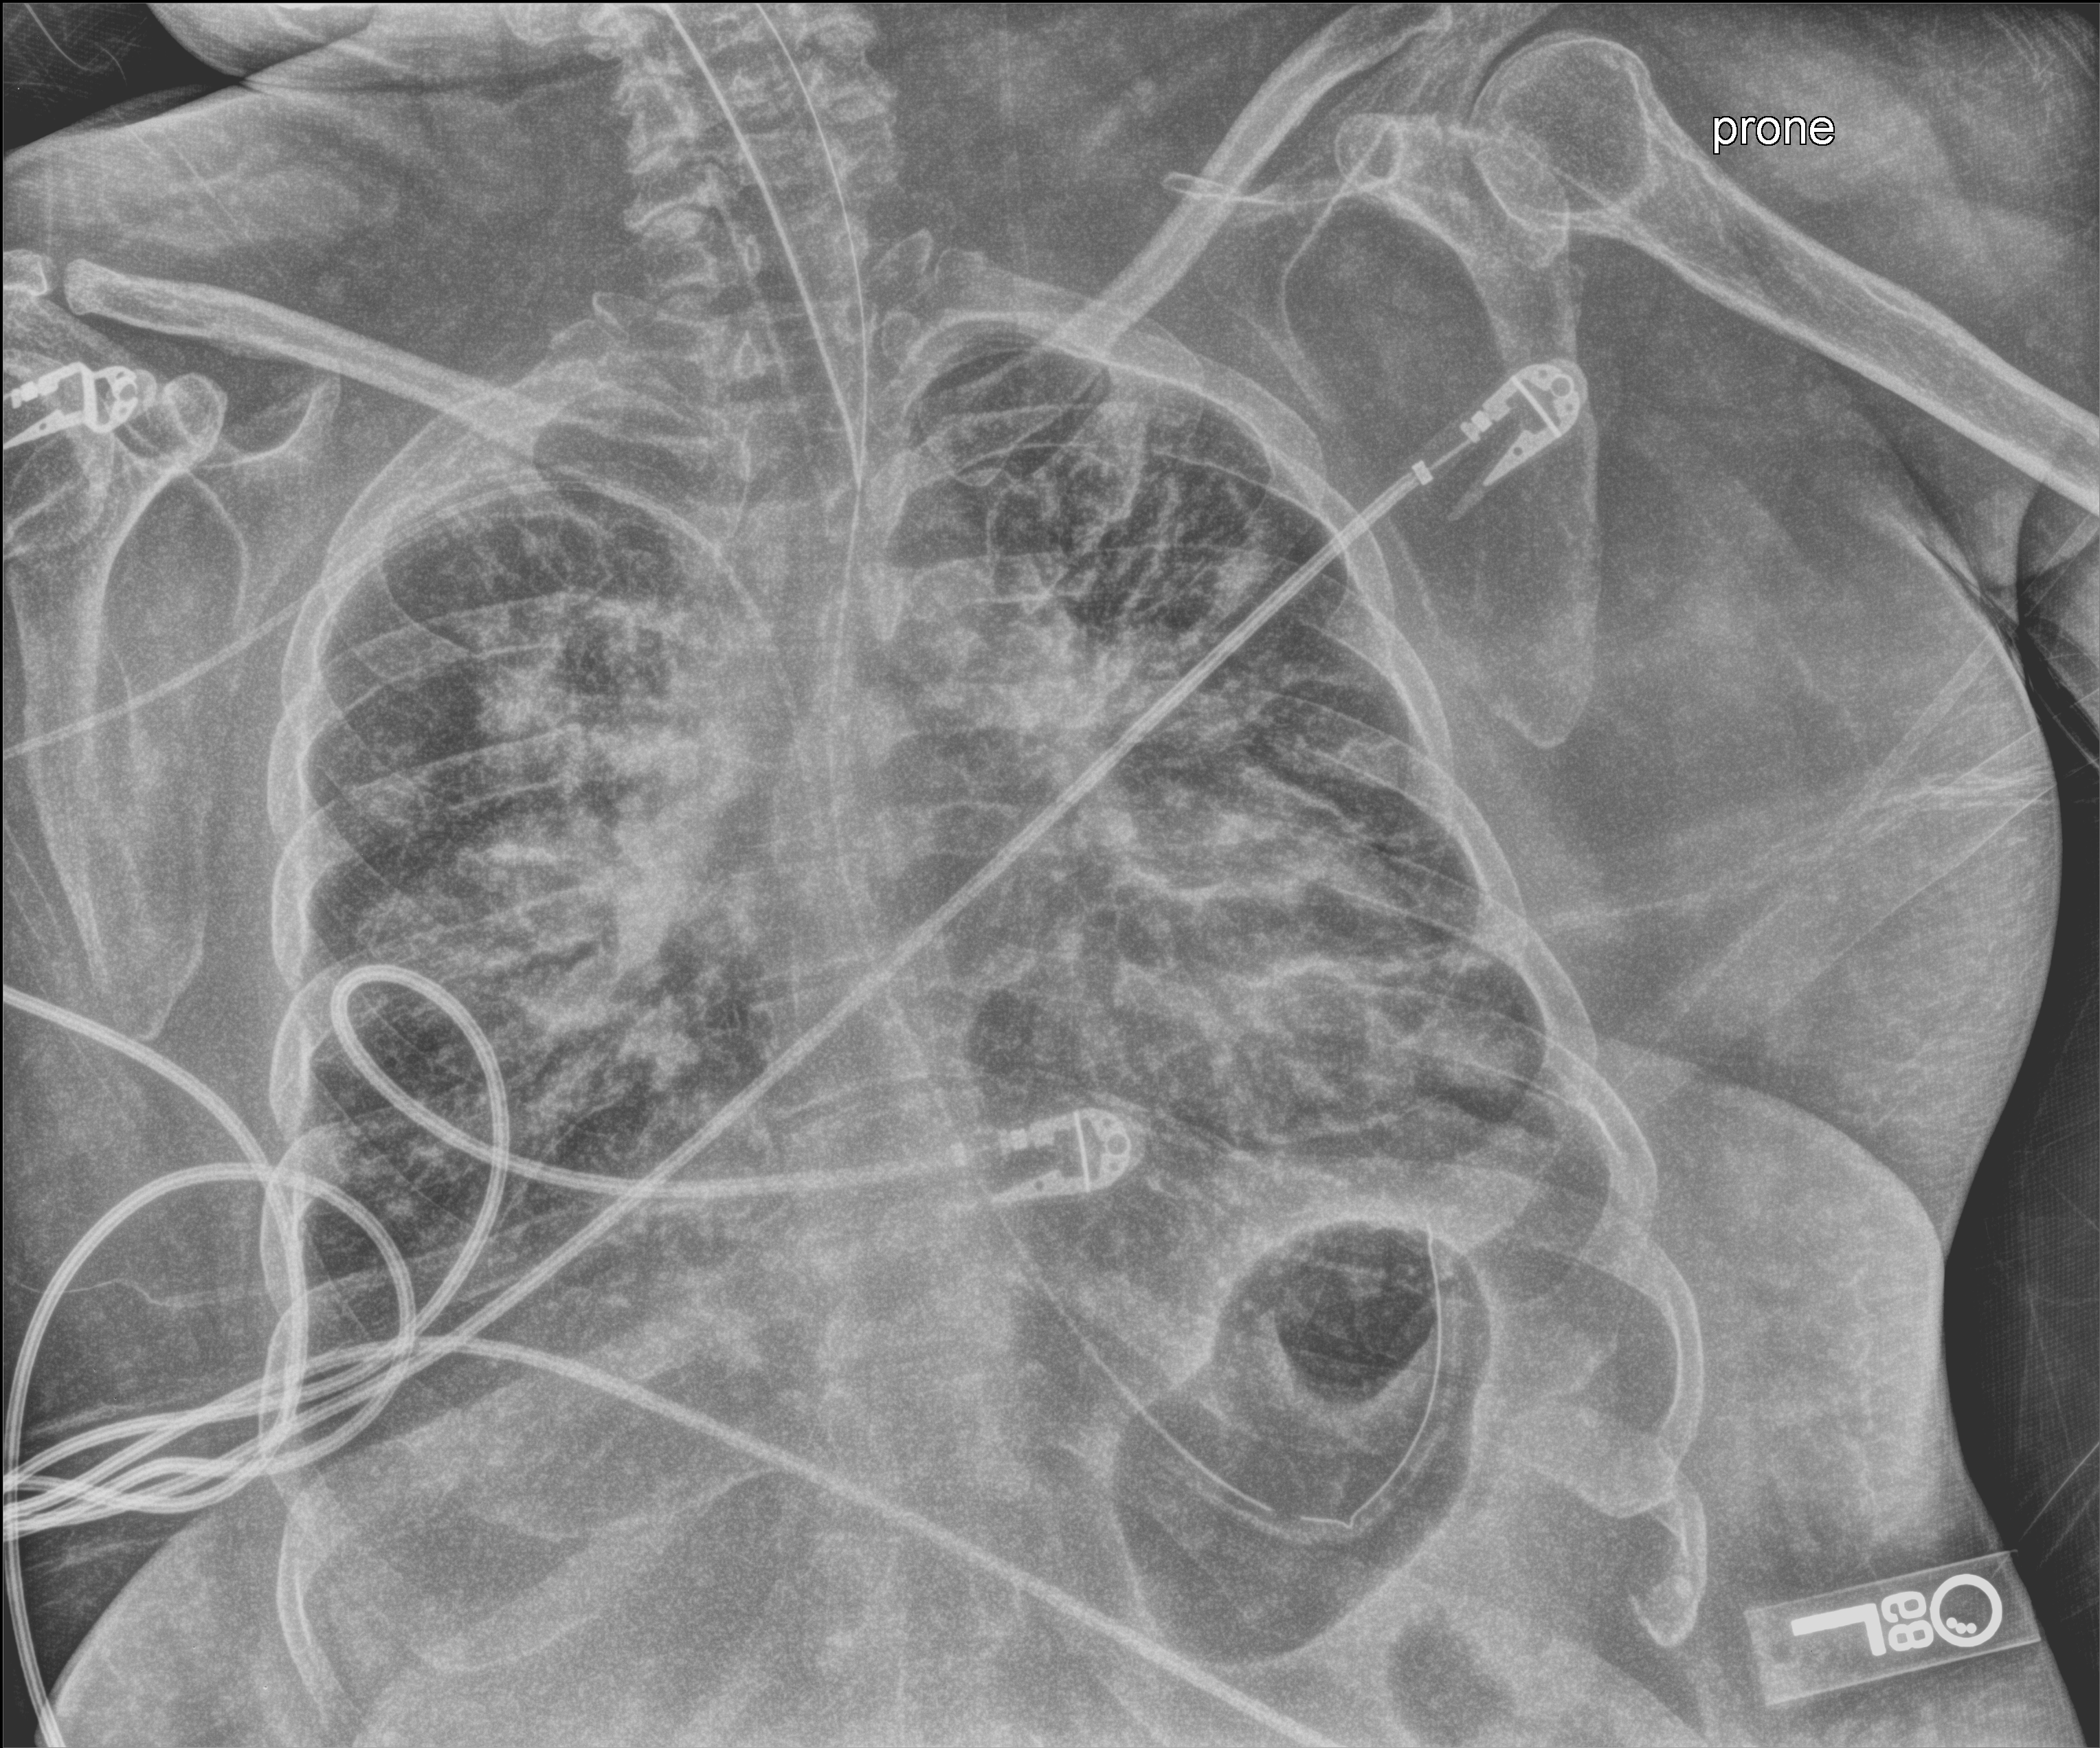
Portable chest radiograph. Adult patient hospitalised with COVID-19, age 18–59 years.
Admission-level facts for this patient (not findings on this image; timing relative to this image not recorded):
- mechanically ventilated during this hospital stay: yes
- admitted to intensive care during this hospital stay: yes